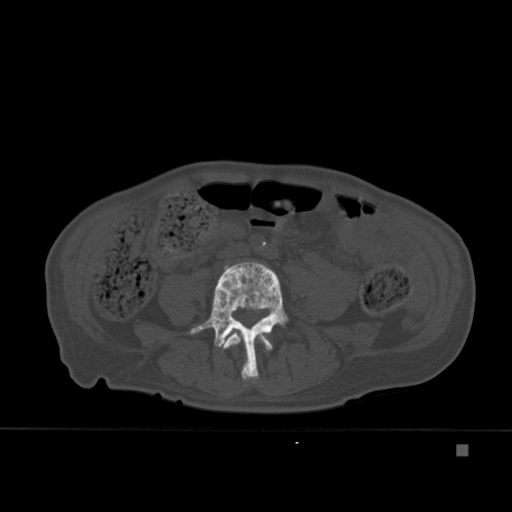
CT including the spine, one axial slice. Slice 125 of 451 in the series (ordered by position). Bone window (W 1800 / L 400 HU). 1.5 mm slice thickness. 512 × 512 image matrix. Patient: male, 75 years. Case-level facts recorded for this patient, not image findings: primary cancer: prostate.
Outlined on this slice (semi-automatically segmented with operator editing):
- L3 vertebra: bounding box [x1, y1, x2, y2] px = [223, 331, 273, 380]
- L4 vertebra: [189, 262, 288, 382]